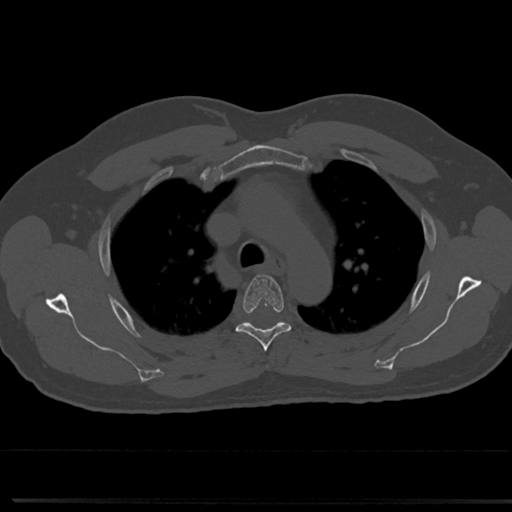
CT including the spine, one axial slice. Position 544 of 817 along the scan axis. Reconstruction kernel Br40s/3. 120 kVp. Bone window (W 1800 / L 400 HU). 512 × 512 image matrix. Patient: male, 61 years. Case-level facts recorded for this patient, not image findings: primary cancer: prostate.
Structures marked on this image (semi-automatic segmentation, software-assisted and operator-edited):
- T4 vertebra: box from (x=234, y=274) to (x=292, y=350) px